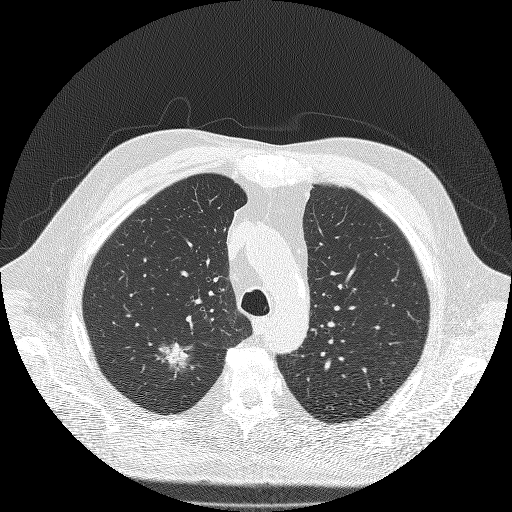
Low-dose screening chest CT, one axial slice. Position 145 of 180 along the scan axis. Reconstruction kernel FC51. 120 kVp. Lung window (W 1500 / L -600 HU). 2 mm slice thickness. 512 × 512 image matrix, field of view 385 × 385 mm.
Structures marked on this image (expert manual segmentation):
- lesion 1 (tumor, upper lobe of right lung): bounding box [x1, y1, x2, y2] px = [159, 343, 189, 378]